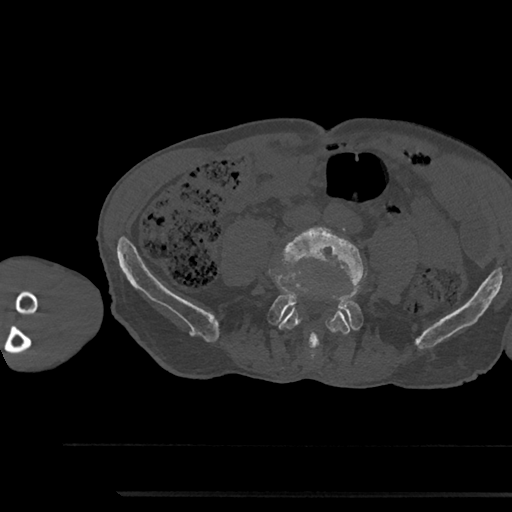
CT including the spine, one axial slice; slice 379 of 797 in the series (ordered by position); reconstruction kernel Br40s/3; bone window (W 1800 / L 400 HU); 512 × 512 image matrix, field of view 367 × 367 mm. Male patient, age 79 years. From the clinical record (not read from this slice): primary cancer: prostate.
Structures marked on this image (semi-automatic segmentation, software-assisted and operator-edited):
- L4 vertebra: bounding box [x1, y1, x2, y2] px = [278, 227, 364, 334]
- L5 vertebra: [270, 292, 362, 347]